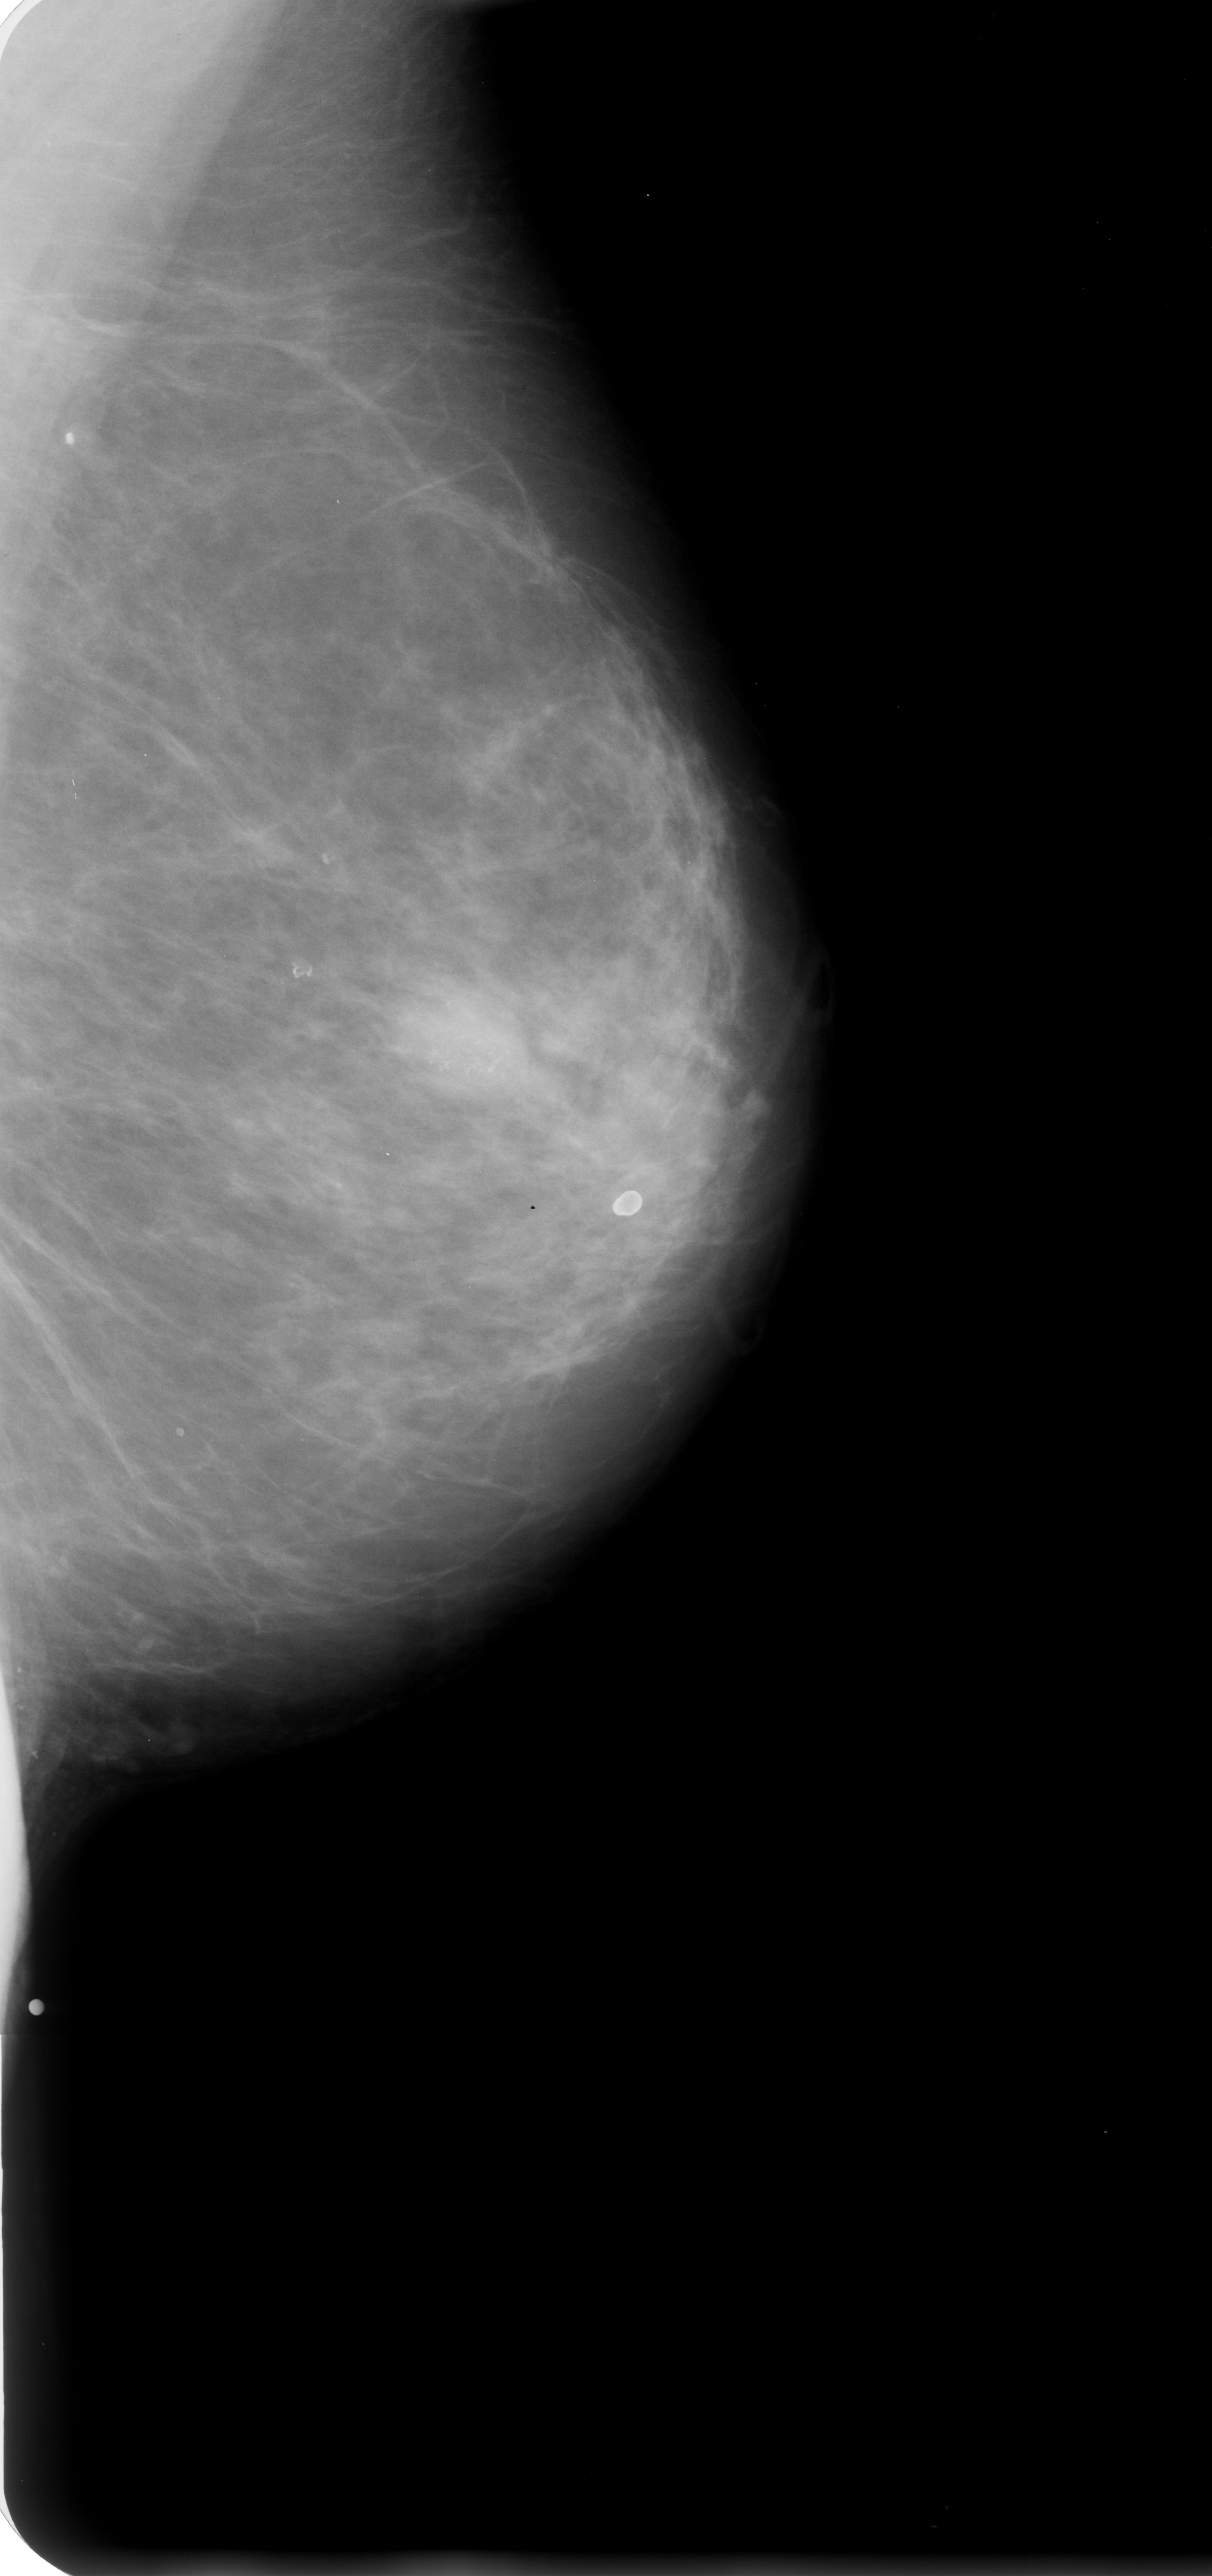
Scanned film-screen mammogram. Left breast. Mediolateral oblique (MLO) view. BI-RADS breast density category 2 (scale 1–4). 1212 × 2576 image matrix.
Expert-marked regions of interest on this film, with their recorded descriptors:
- calcifications, morphology pleomorphic, distribution clustered; BI-RADS assessment category 4; subtlety rating 4 on a 1 (subtle) to 5 (obvious) scale; pathology (as recorded): benign: bounding box <388,970,536,1106> (left, top, right, bottom; pixels)